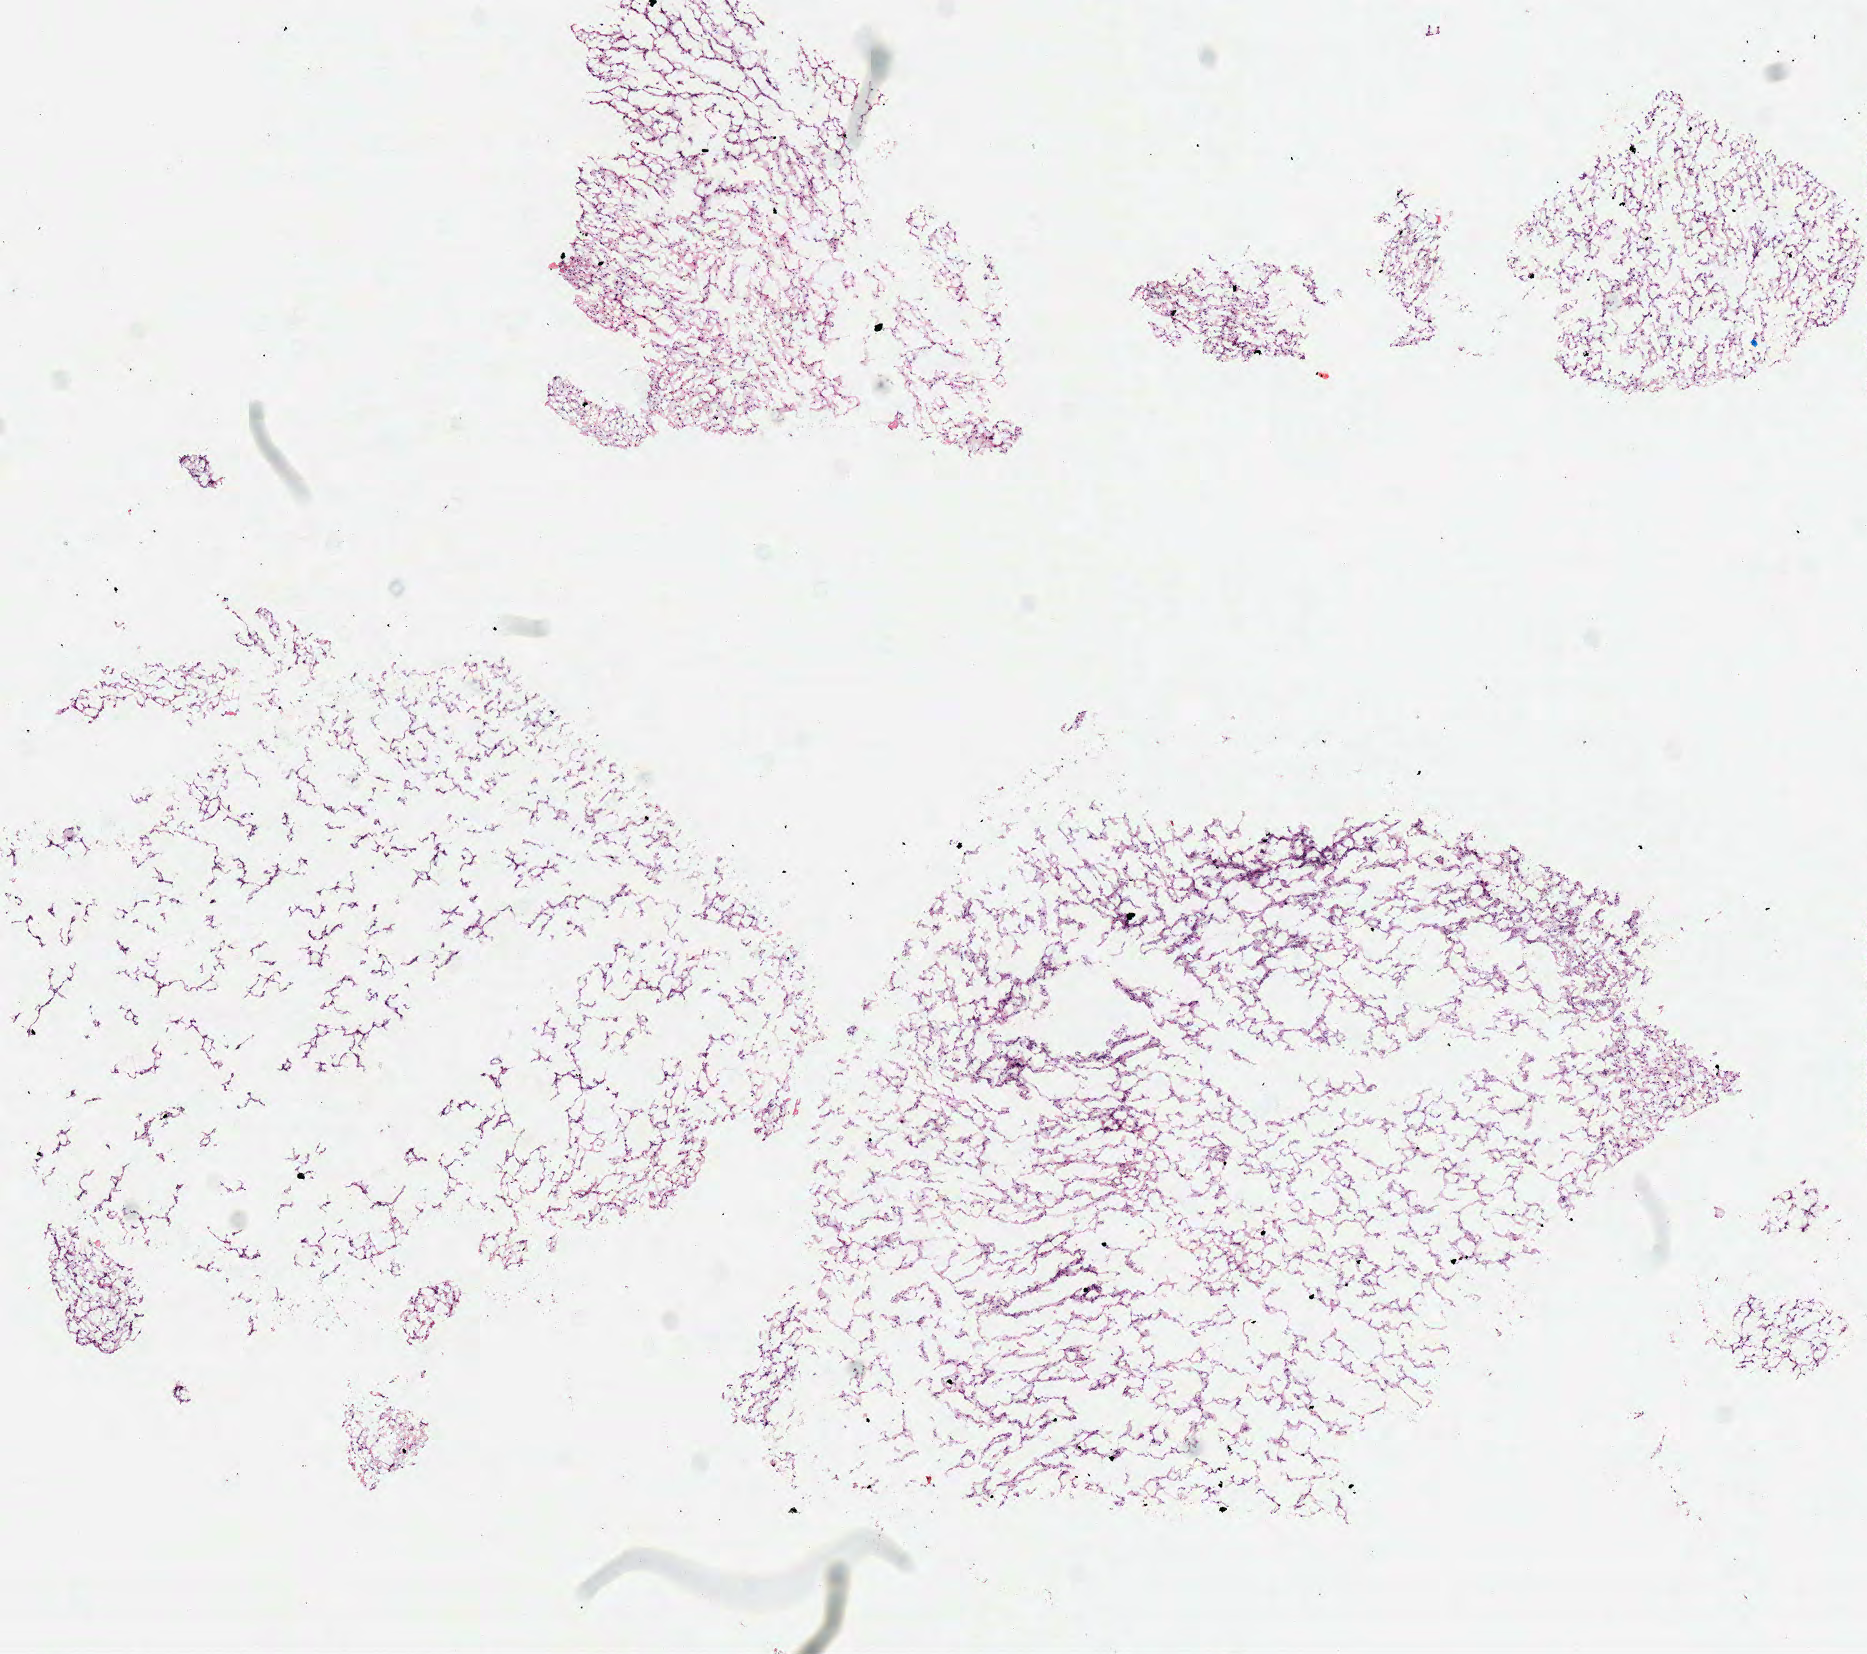
H&E-stained whole-slide image, a low-resolution overview of the entire scanned area, about 7.3 x 6.5 mm, frozen section from the top of the tissue portion, sample: primary tumour, brain. Female patient; age at initial diagnosis 23 years. Histologic grade: G2 (moderately differentiated). Pathologist review of this section (percent, as recorded): tumour cells 100%, tumour nuclei 70%, normal cells 0%, stromal cells 0%, necrosis 0%.
Laterality: right. Pathologic diagnosis: Astrocytoma, NOS (cerebrum).